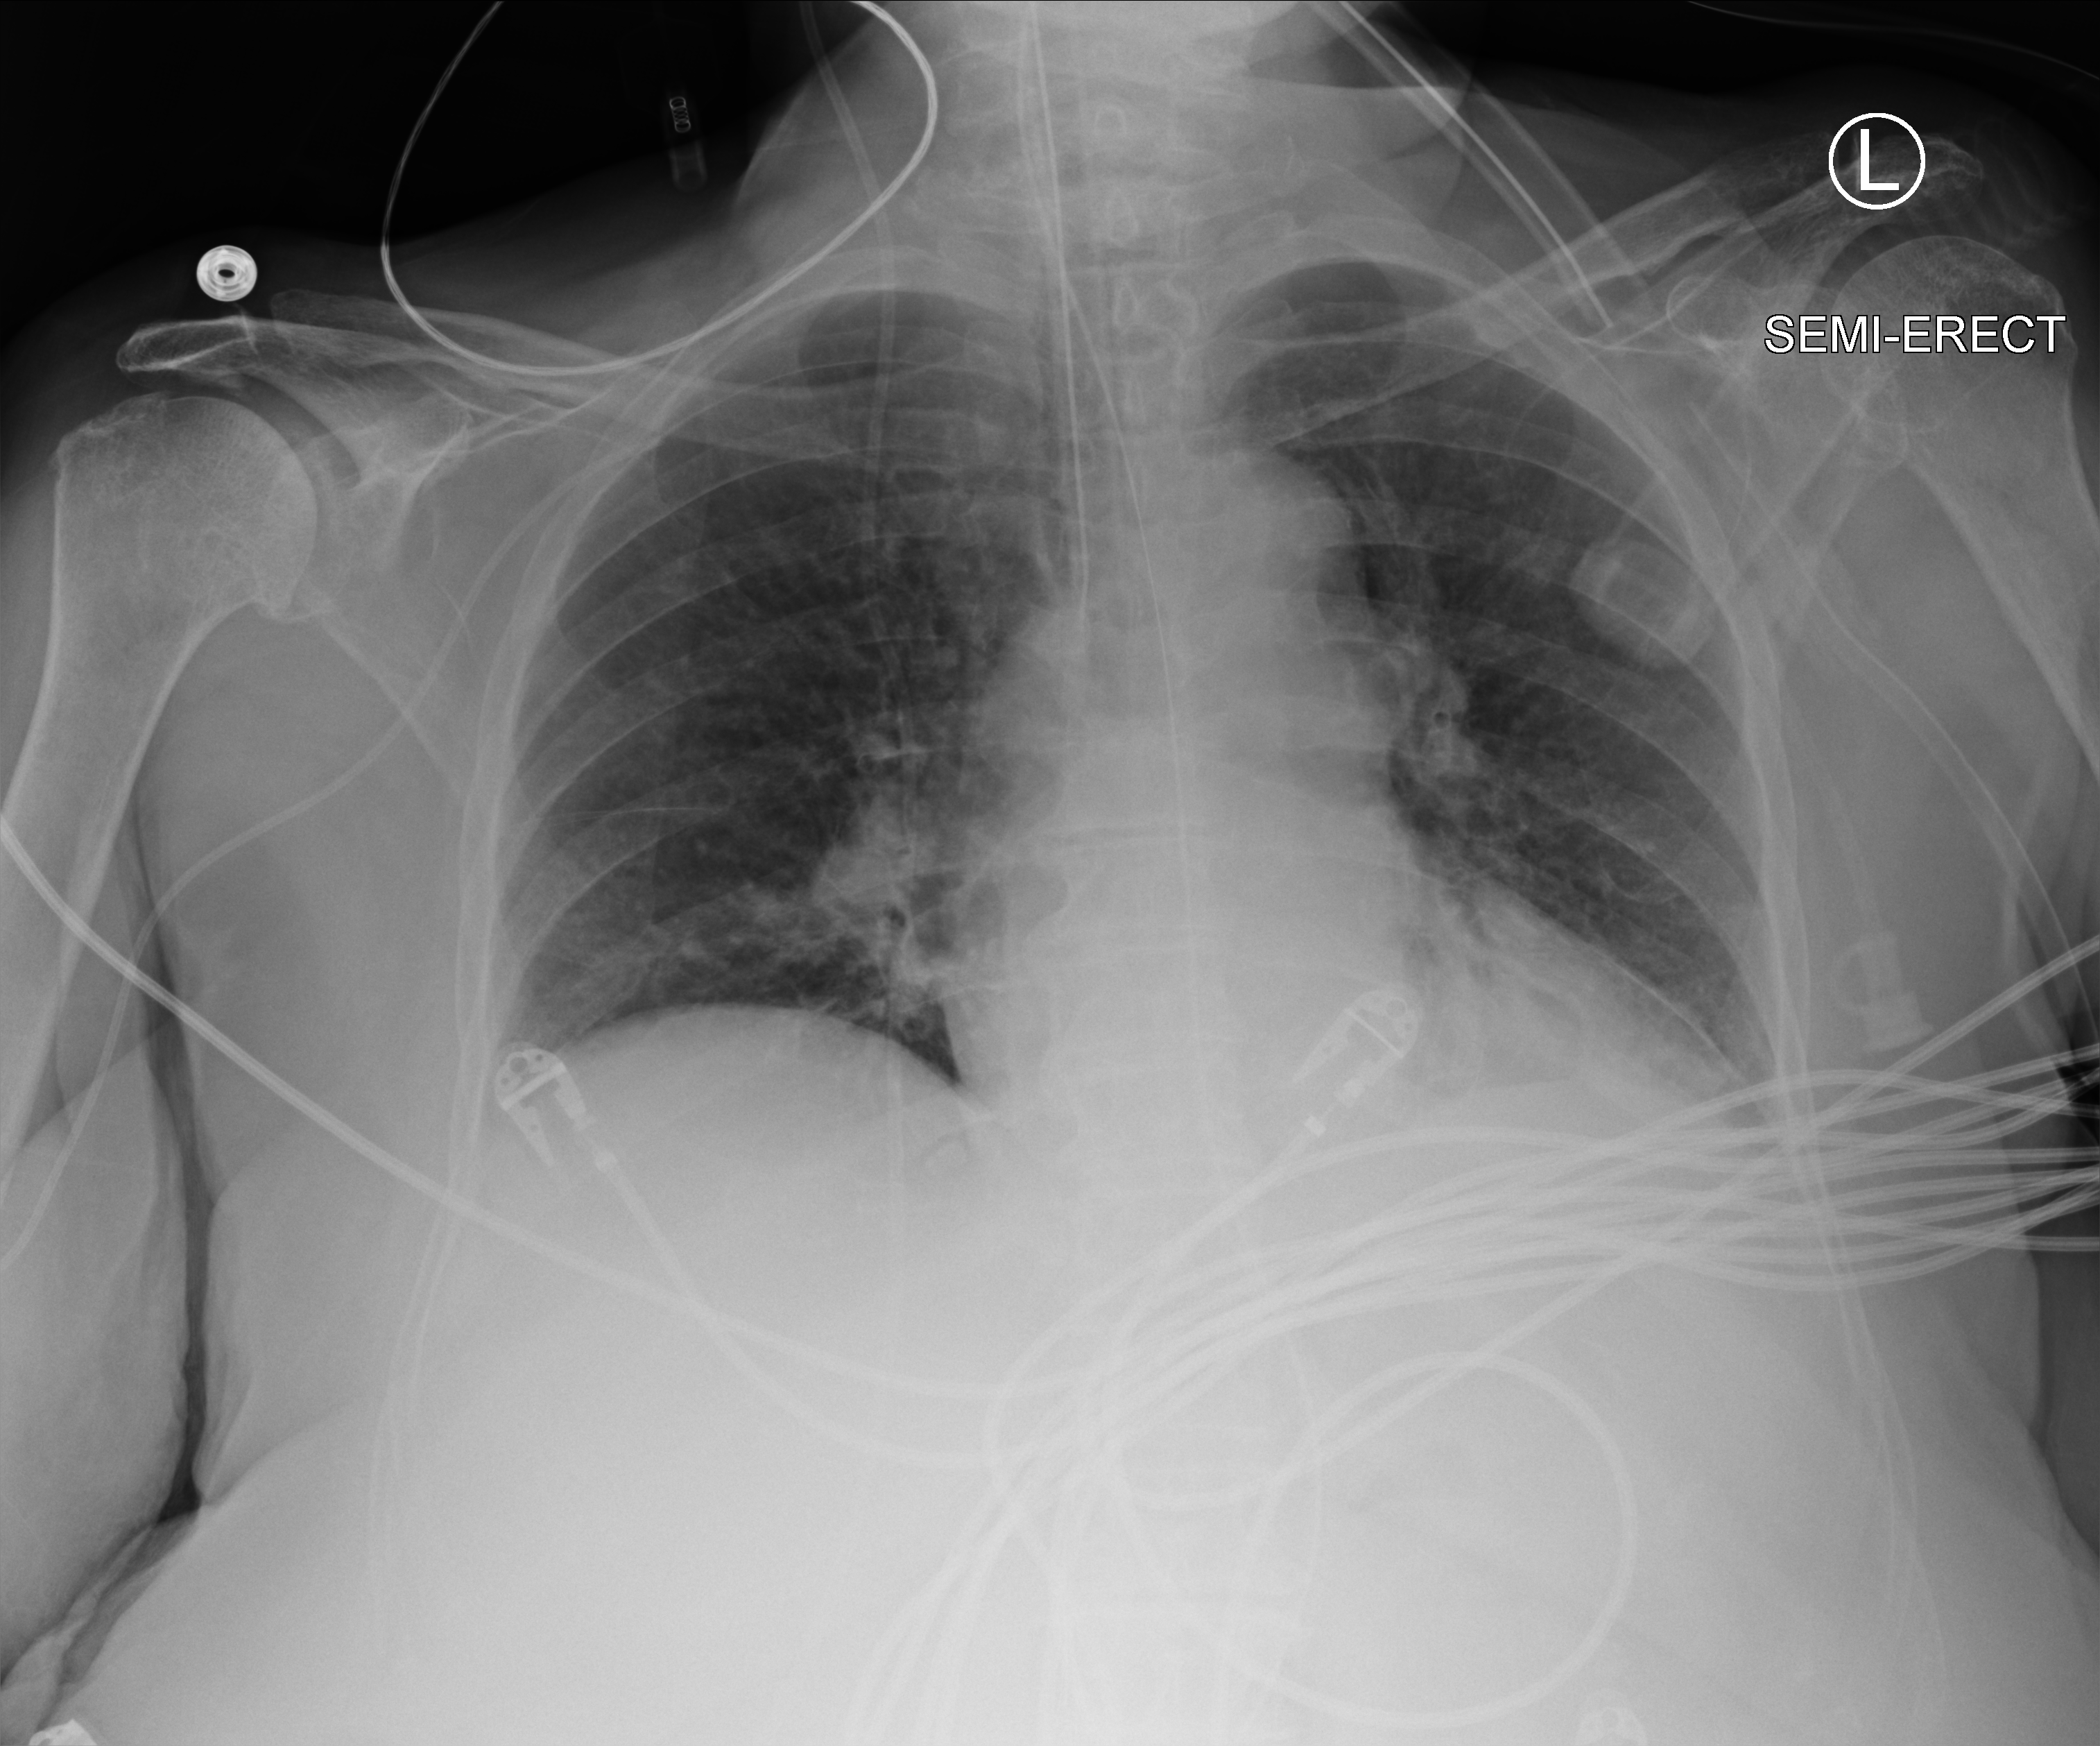
Chest X-ray (portable), anteroposterior (AP) projection. Patient hospitalised with COVID-19; female, aged 75–90 years.
Hospital-stay facts (about this admission, not read from this image; timing relative to this image not recorded): length of hospital stay: 29 days.